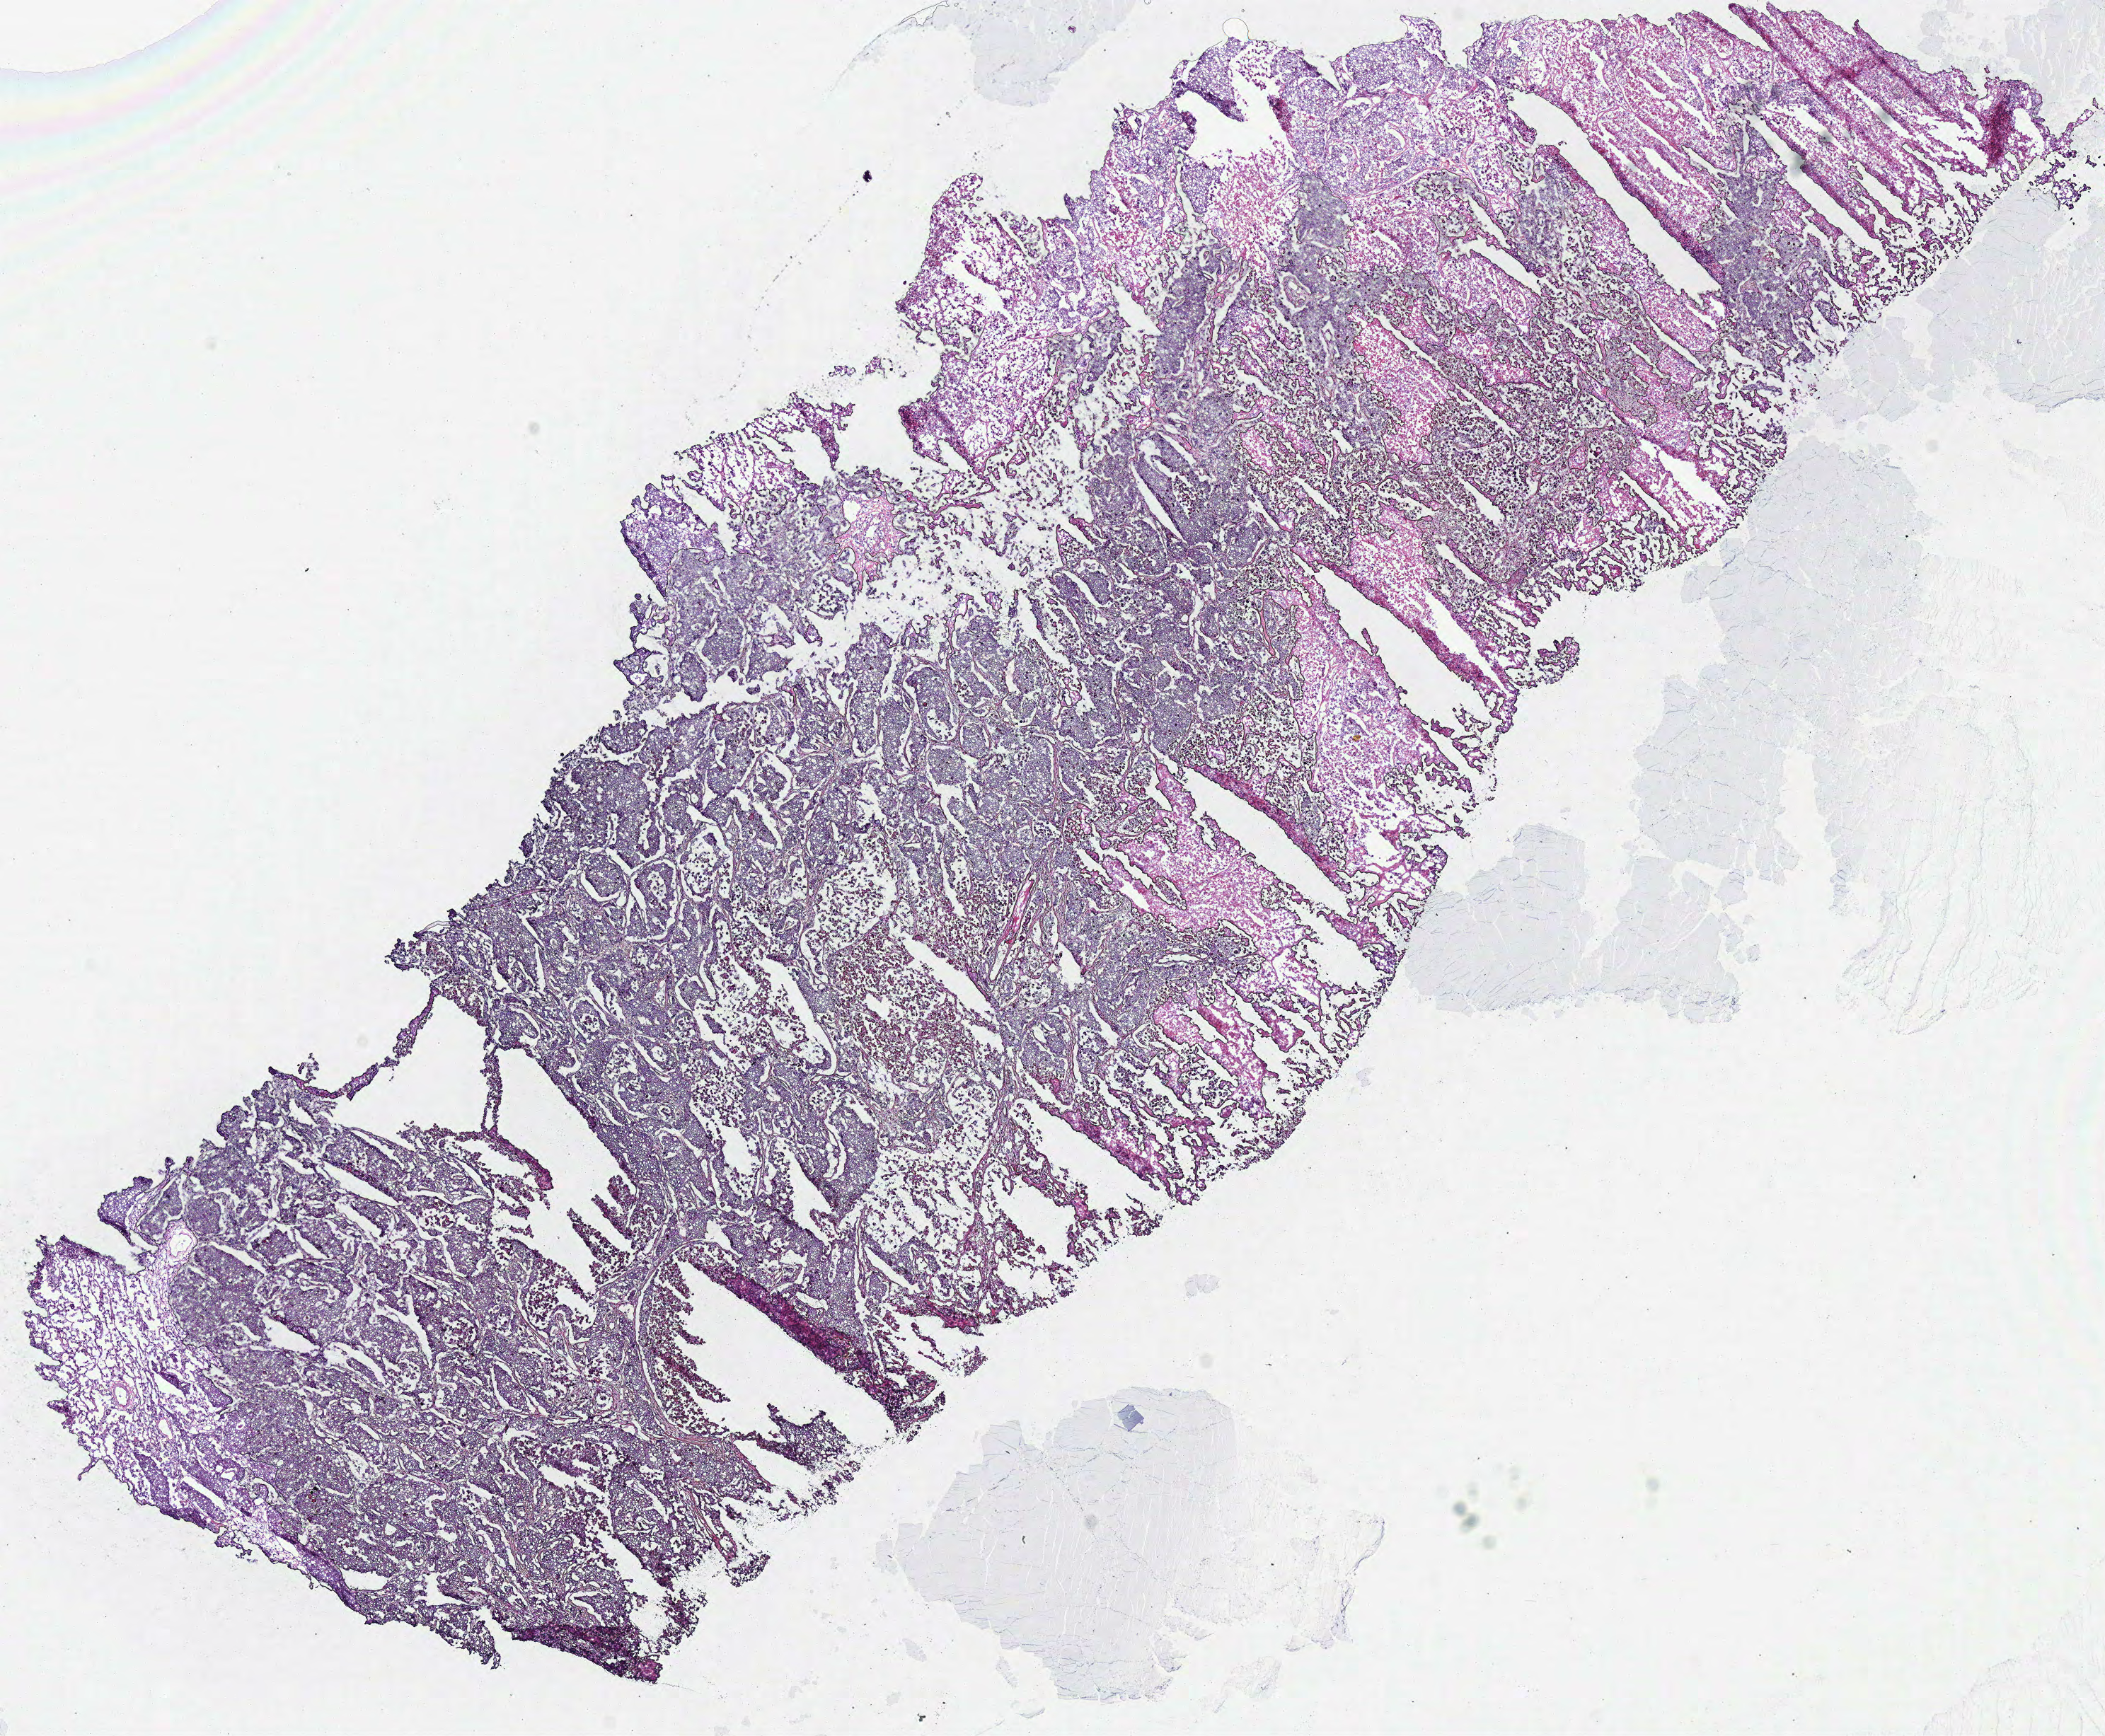
Digitized Hematoxylin and eosin (H&E) stained tissue section (whole slide) — shown as a low-resolution overview of the whole scanned area (about 11.7 x 9.7 mm). Frozen section. Lung, primary tumour sample. Male patient; age at initial diagnosis 71 years. Composition of this section per pathologist review: tumour cells 70%, tumour nuclei 80%.
Pathologic diagnosis: Squamous cell carcinoma, NOS.